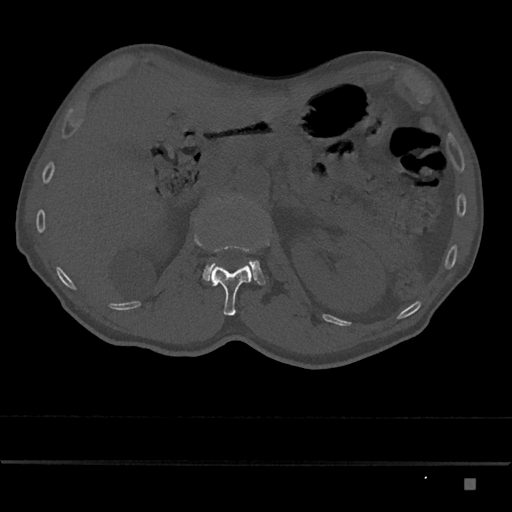
CT including the spine, one axial slice; position 523 of 797 along the scan axis; 120 kVp; bone window (W 1800 / L 400 HU); 0.5 mm slice thickness; 512 × 512 image matrix, field of view 390 × 390 mm. Patient: male, 72 years. From the clinical record (not read from this slice): primary cancer: prostate.
Outlined on this slice (semi-automatically segmented with operator editing):
- L1 vertebra: box from (x=210, y=242) to (x=268, y=316) px
- L2 vertebra: (x=202, y=196)–(x=266, y=285)